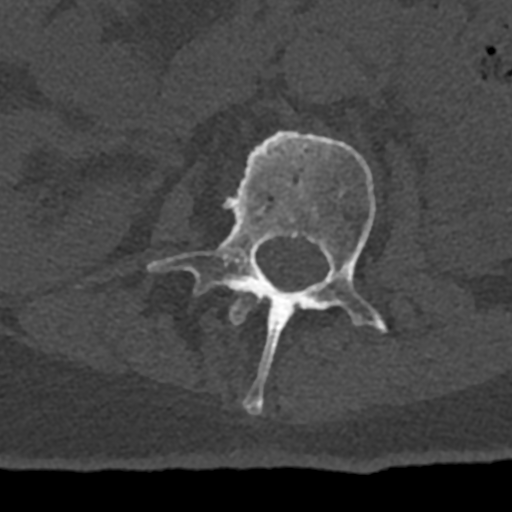
CT including the spine, one axial slice. Slice 382 of 797 in the series (ordered by position). 120 kVp. Bone window (W 1800 / L 400 HU). 512 × 512 image matrix, field of view 160 × 160 mm. Patient: male, 74 years. Case-level facts recorded for this patient, not image findings: primary cancer: renal; vertebrae with lytic lesions (as recorded): T10, L1, L2, L3, L4, L5.
Annotated regions visible in this slice (semi-automatically segmented with operator editing):
- L1 vertebra: bounding box <229,291,250,325> (left, top, right, bottom; pixels)
- L2 vertebra: <147,131,388,414>